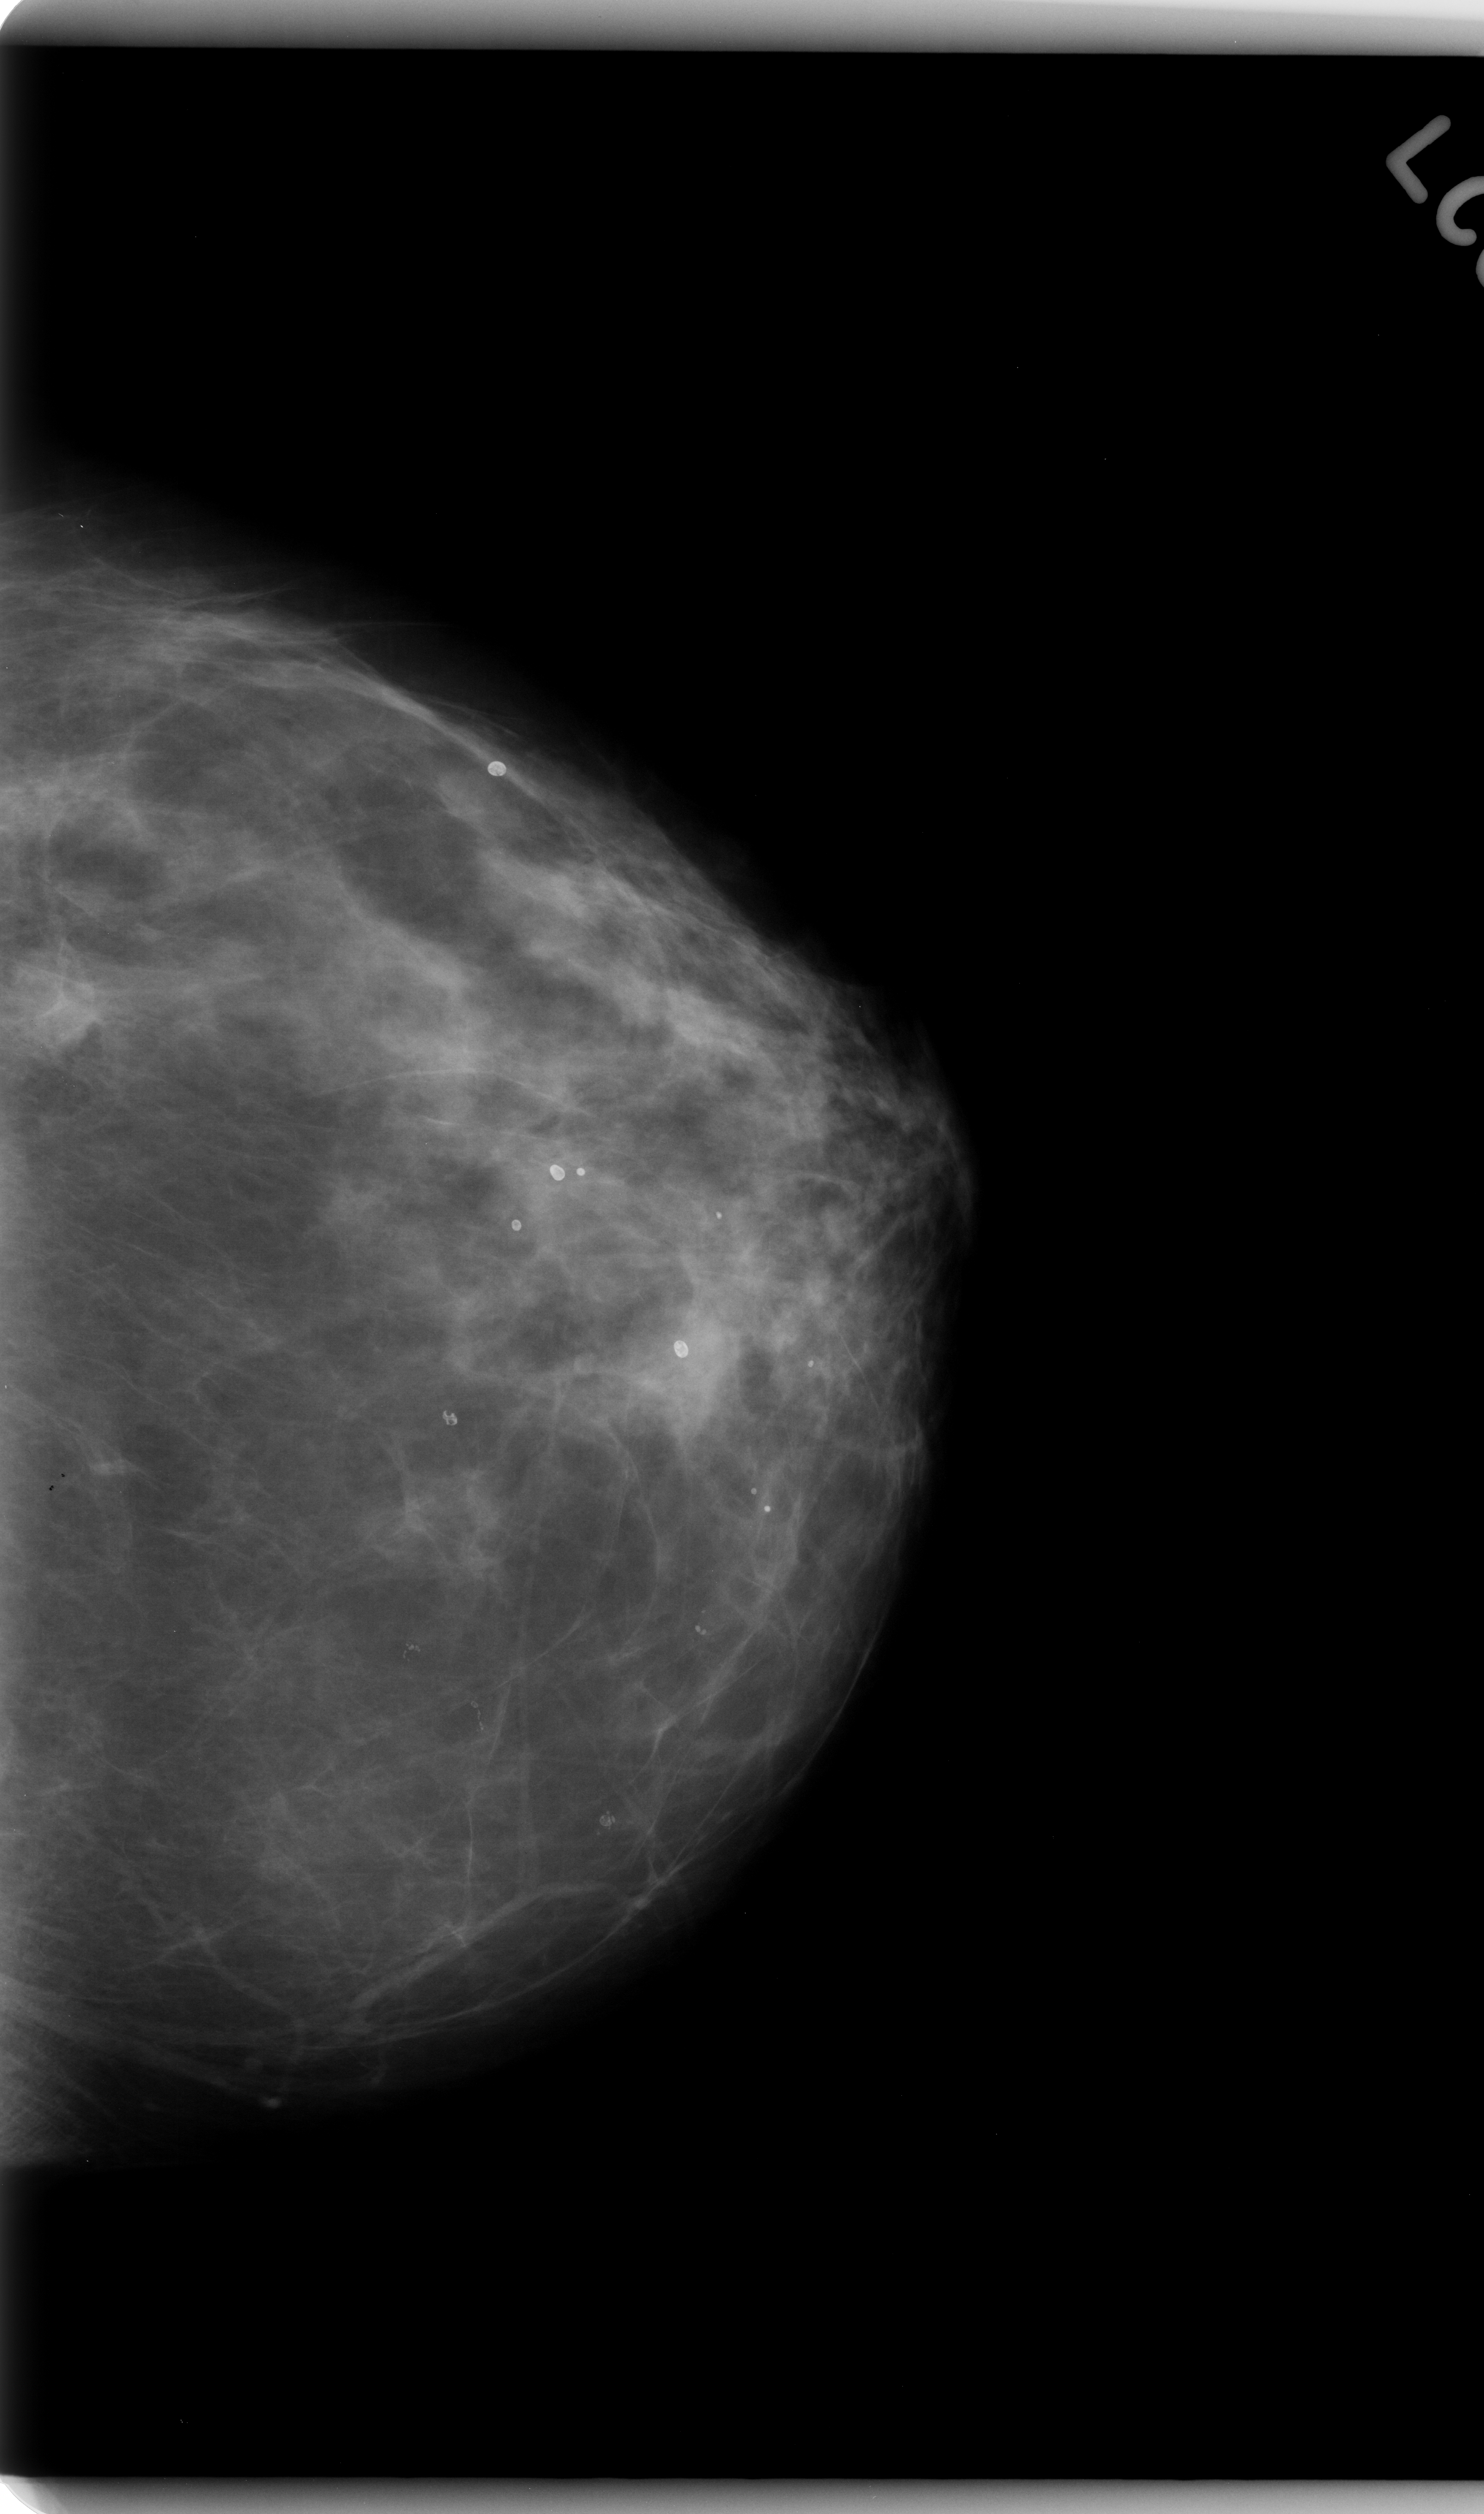
Scanned film-screen mammogram; left breast; craniocaudal (CC) view; 1484 × 2514 image matrix.
Marked abnormalities (boxes around the expert regions of interest):
- mass, shape lobulated, margins ill defined; BI-RADS assessment category 5; subtlety rating 4 on a 1 (subtle) to 5 (obvious) scale; pathology (as recorded): malignant: bounding box <13,935,141,1081> (left, top, right, bottom; pixels)